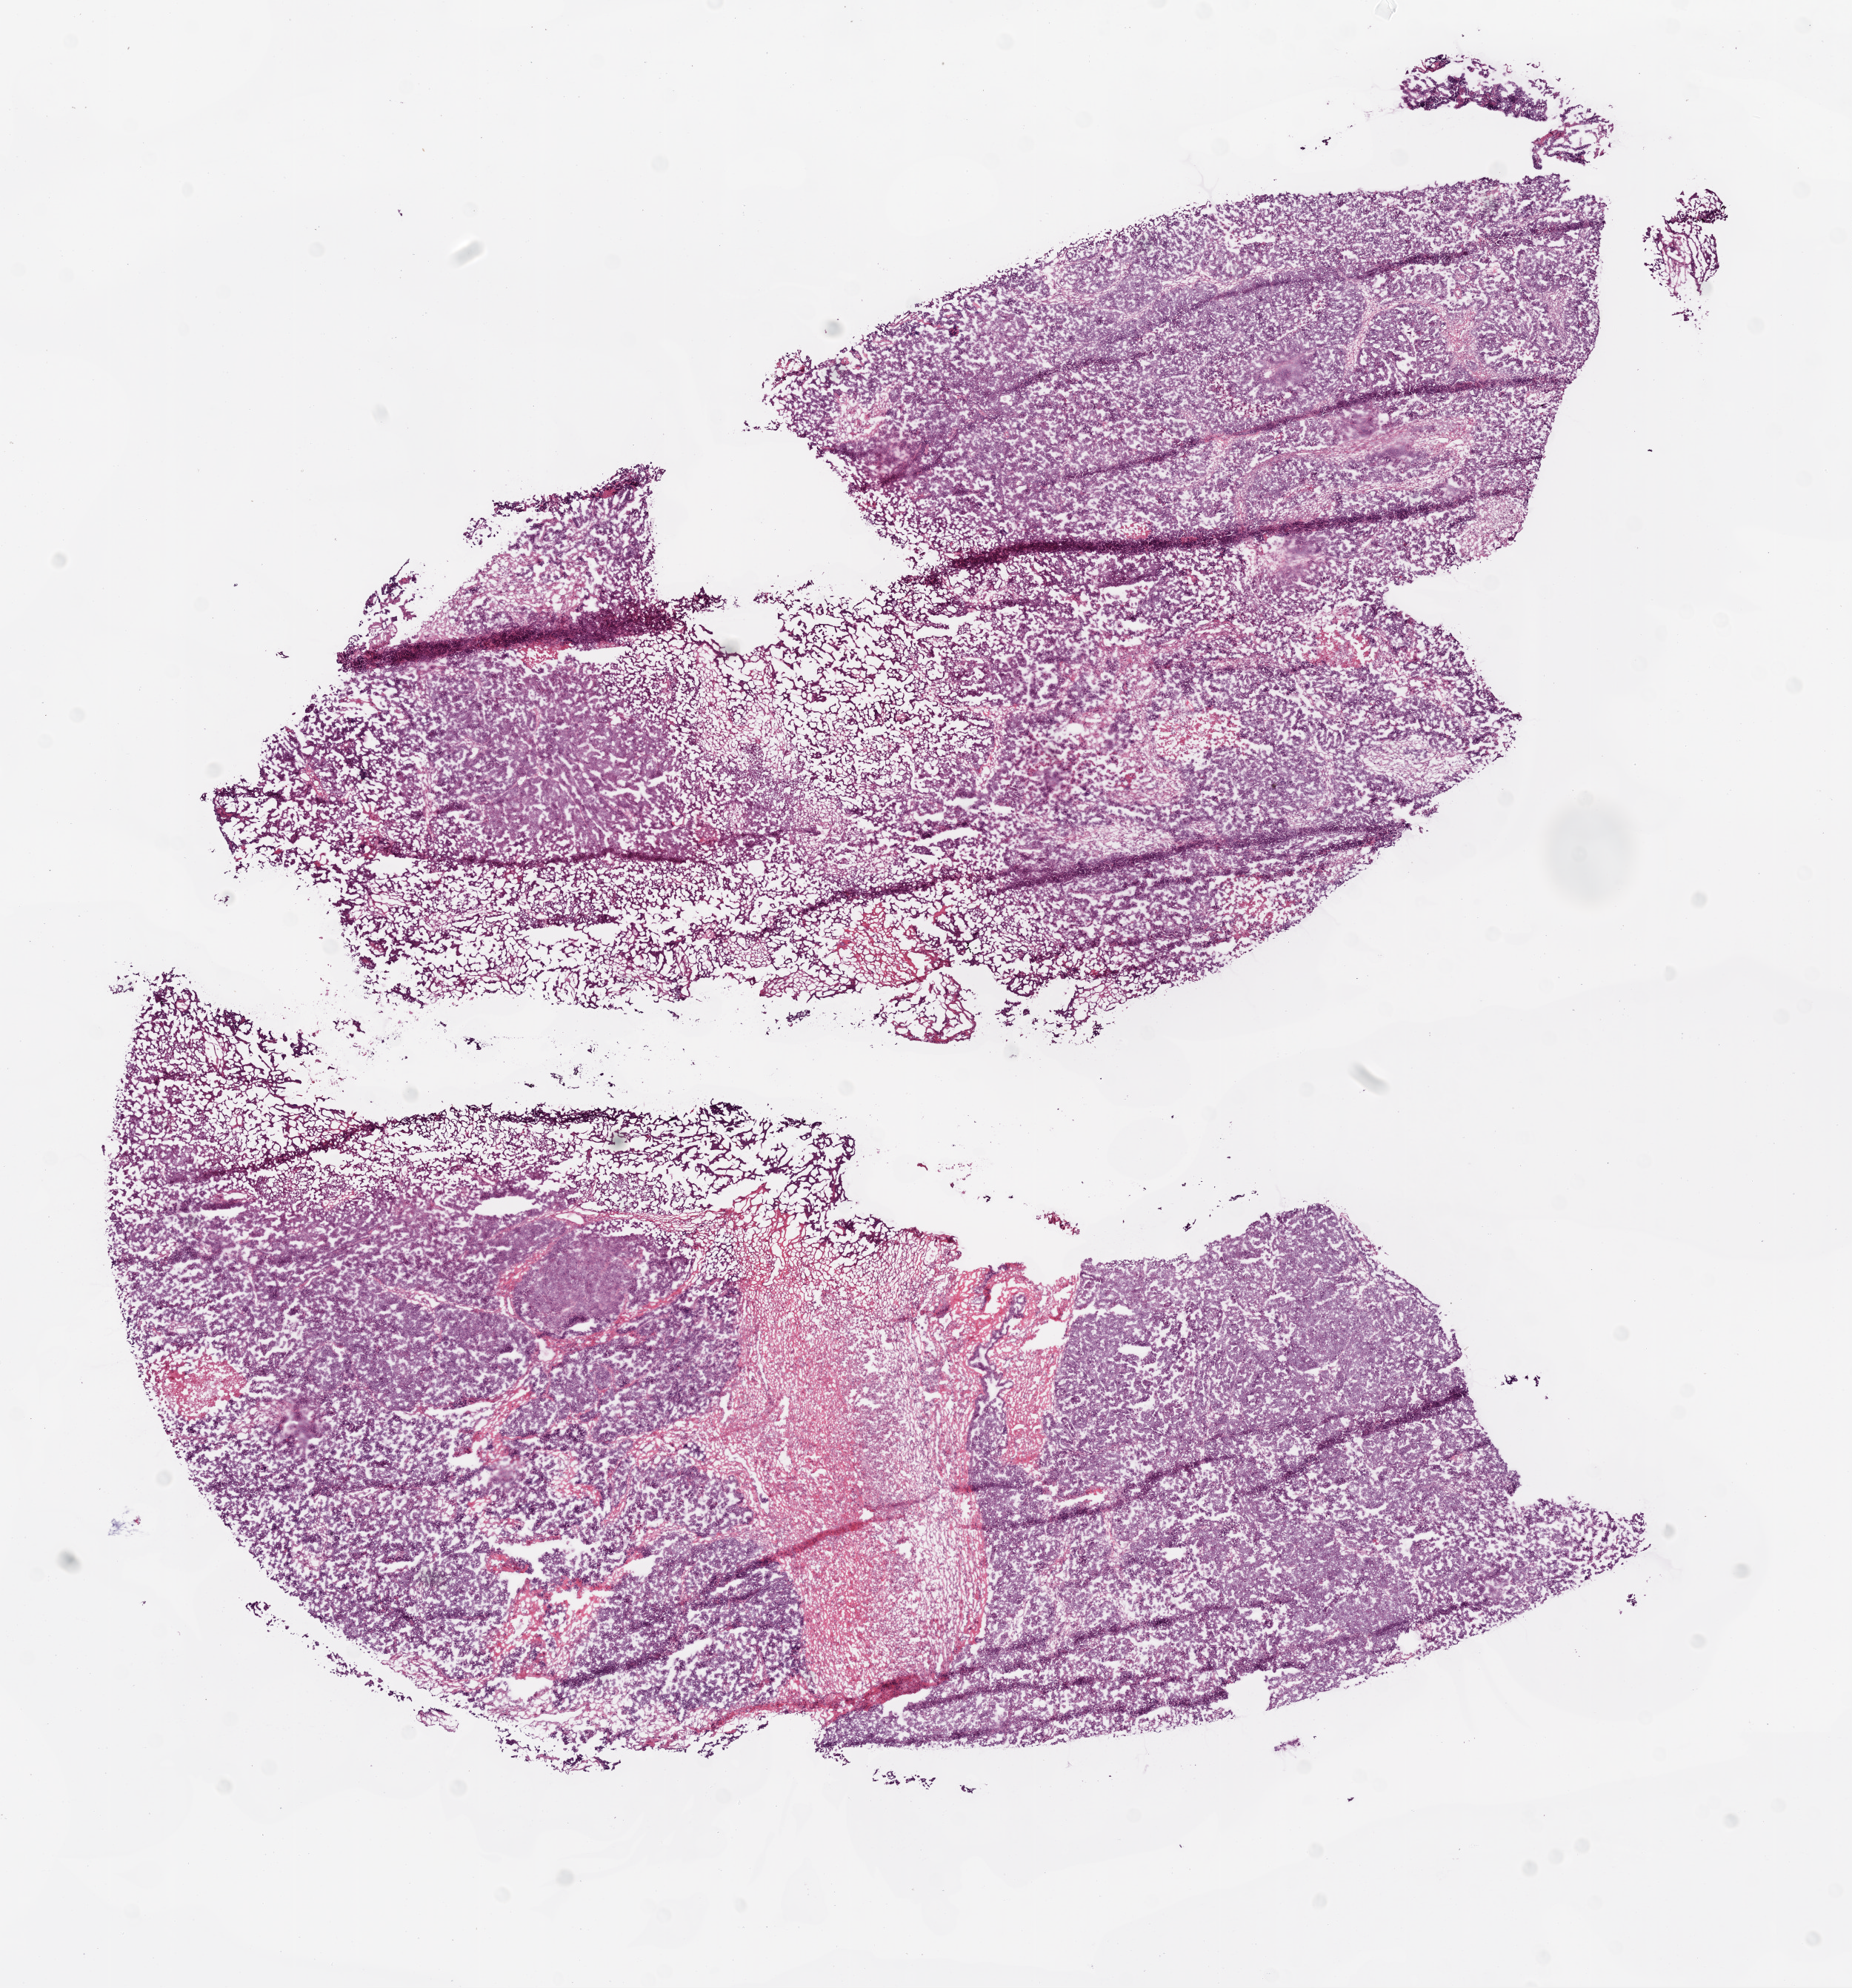
H&E whole-slide image, shown as a low-resolution overview of the whole scanned area (about 10.0 x 10.8 mm, acquisition: 20x scan), frozen section from the top of the tissue portion, sample: primary tumour, ovary. Female, age 51 years at initial diagnosis. Histologic grade: G3 (poorly differentiated). Composition of this section per pathologist review: tumour cells 85%, tumour nuclei 85%, normal cells 5%, stromal cells 0%, necrosis 10%.
Laterality: bilateral. FIGO stage: IIIC. Histologic diagnosis: Serous cystadenocarcinoma, NOS.